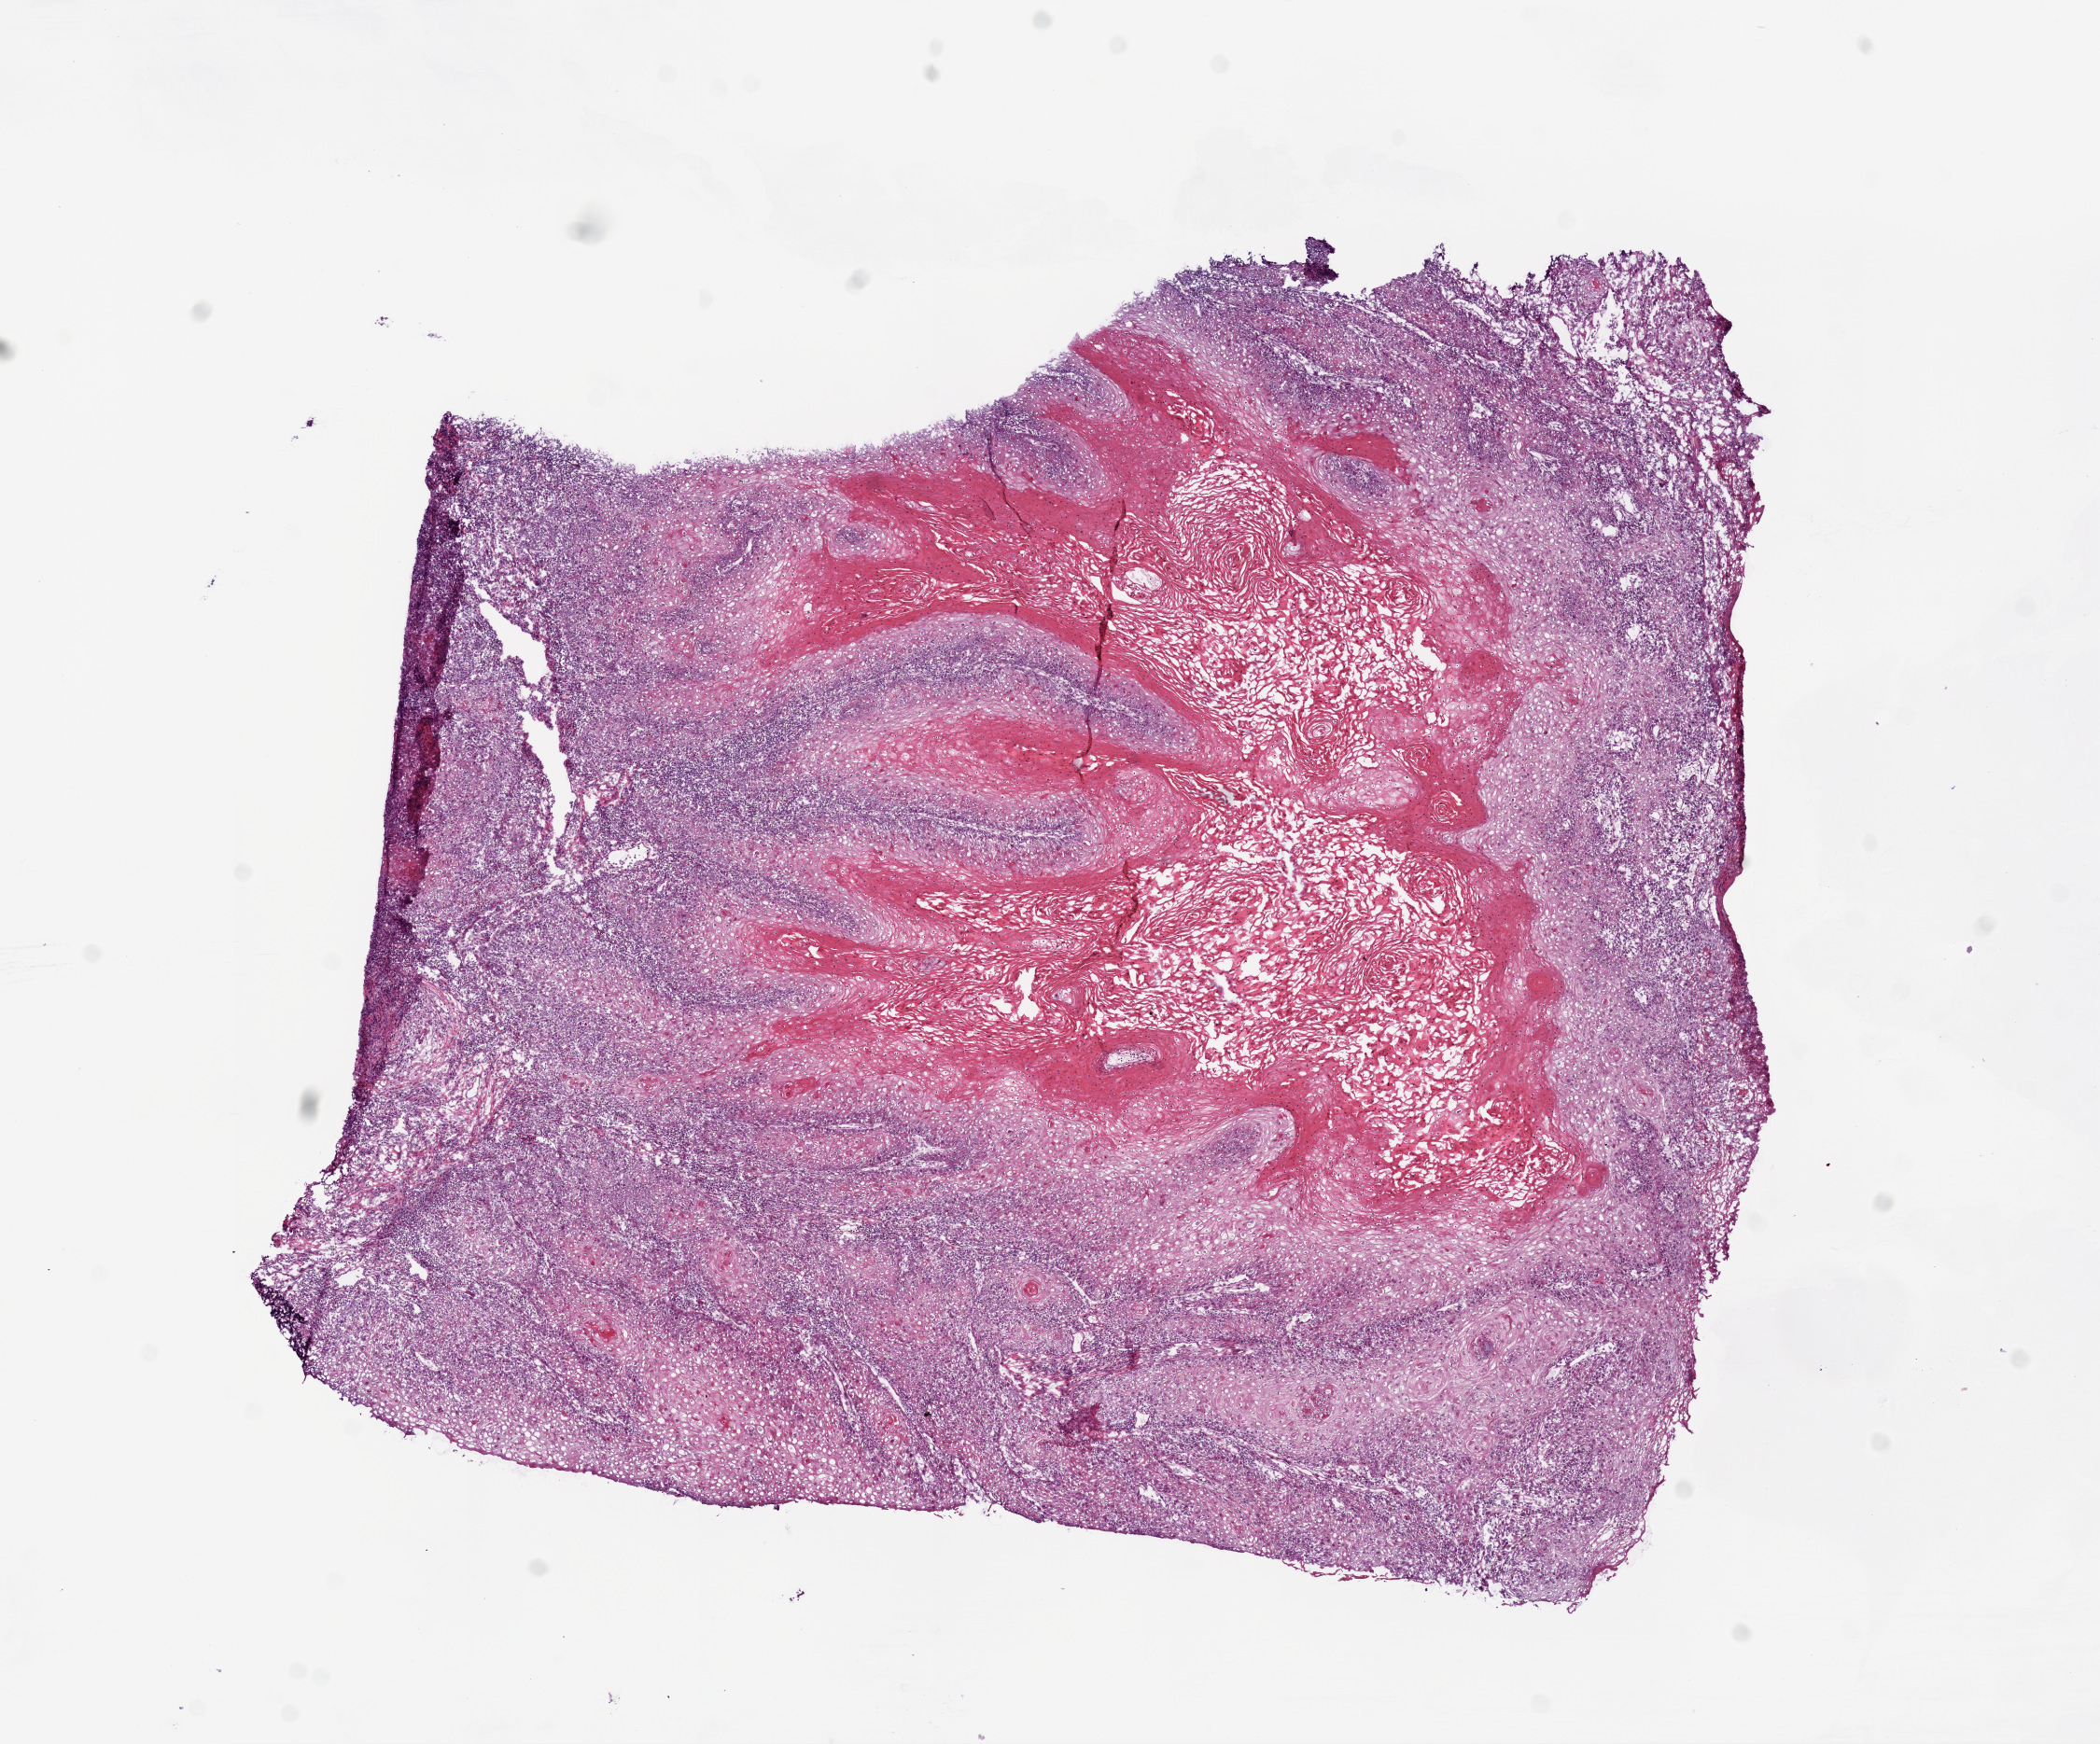
Whole-slide histology image, H&E-stained — shown as a low-resolution overview of the whole scanned area (about 9.0 x 7.5 mm); frozen section; head and neck, primary tumour sample. Patient: female, age at initial diagnosis 73 years. Histologic grade: G2 (moderately differentiated). Slide review estimates, as recorded: tumour cells 95%, tumour nuclei 70%, normal cells 0%, stromal cells 5%, necrosis 0%. Infiltration values recorded for this section: lymphocyte infiltration 25%, monocyte infiltration 0%, neutrophil infiltration 0%.
Histologic diagnosis: Squamous cell carcinoma, NOS.